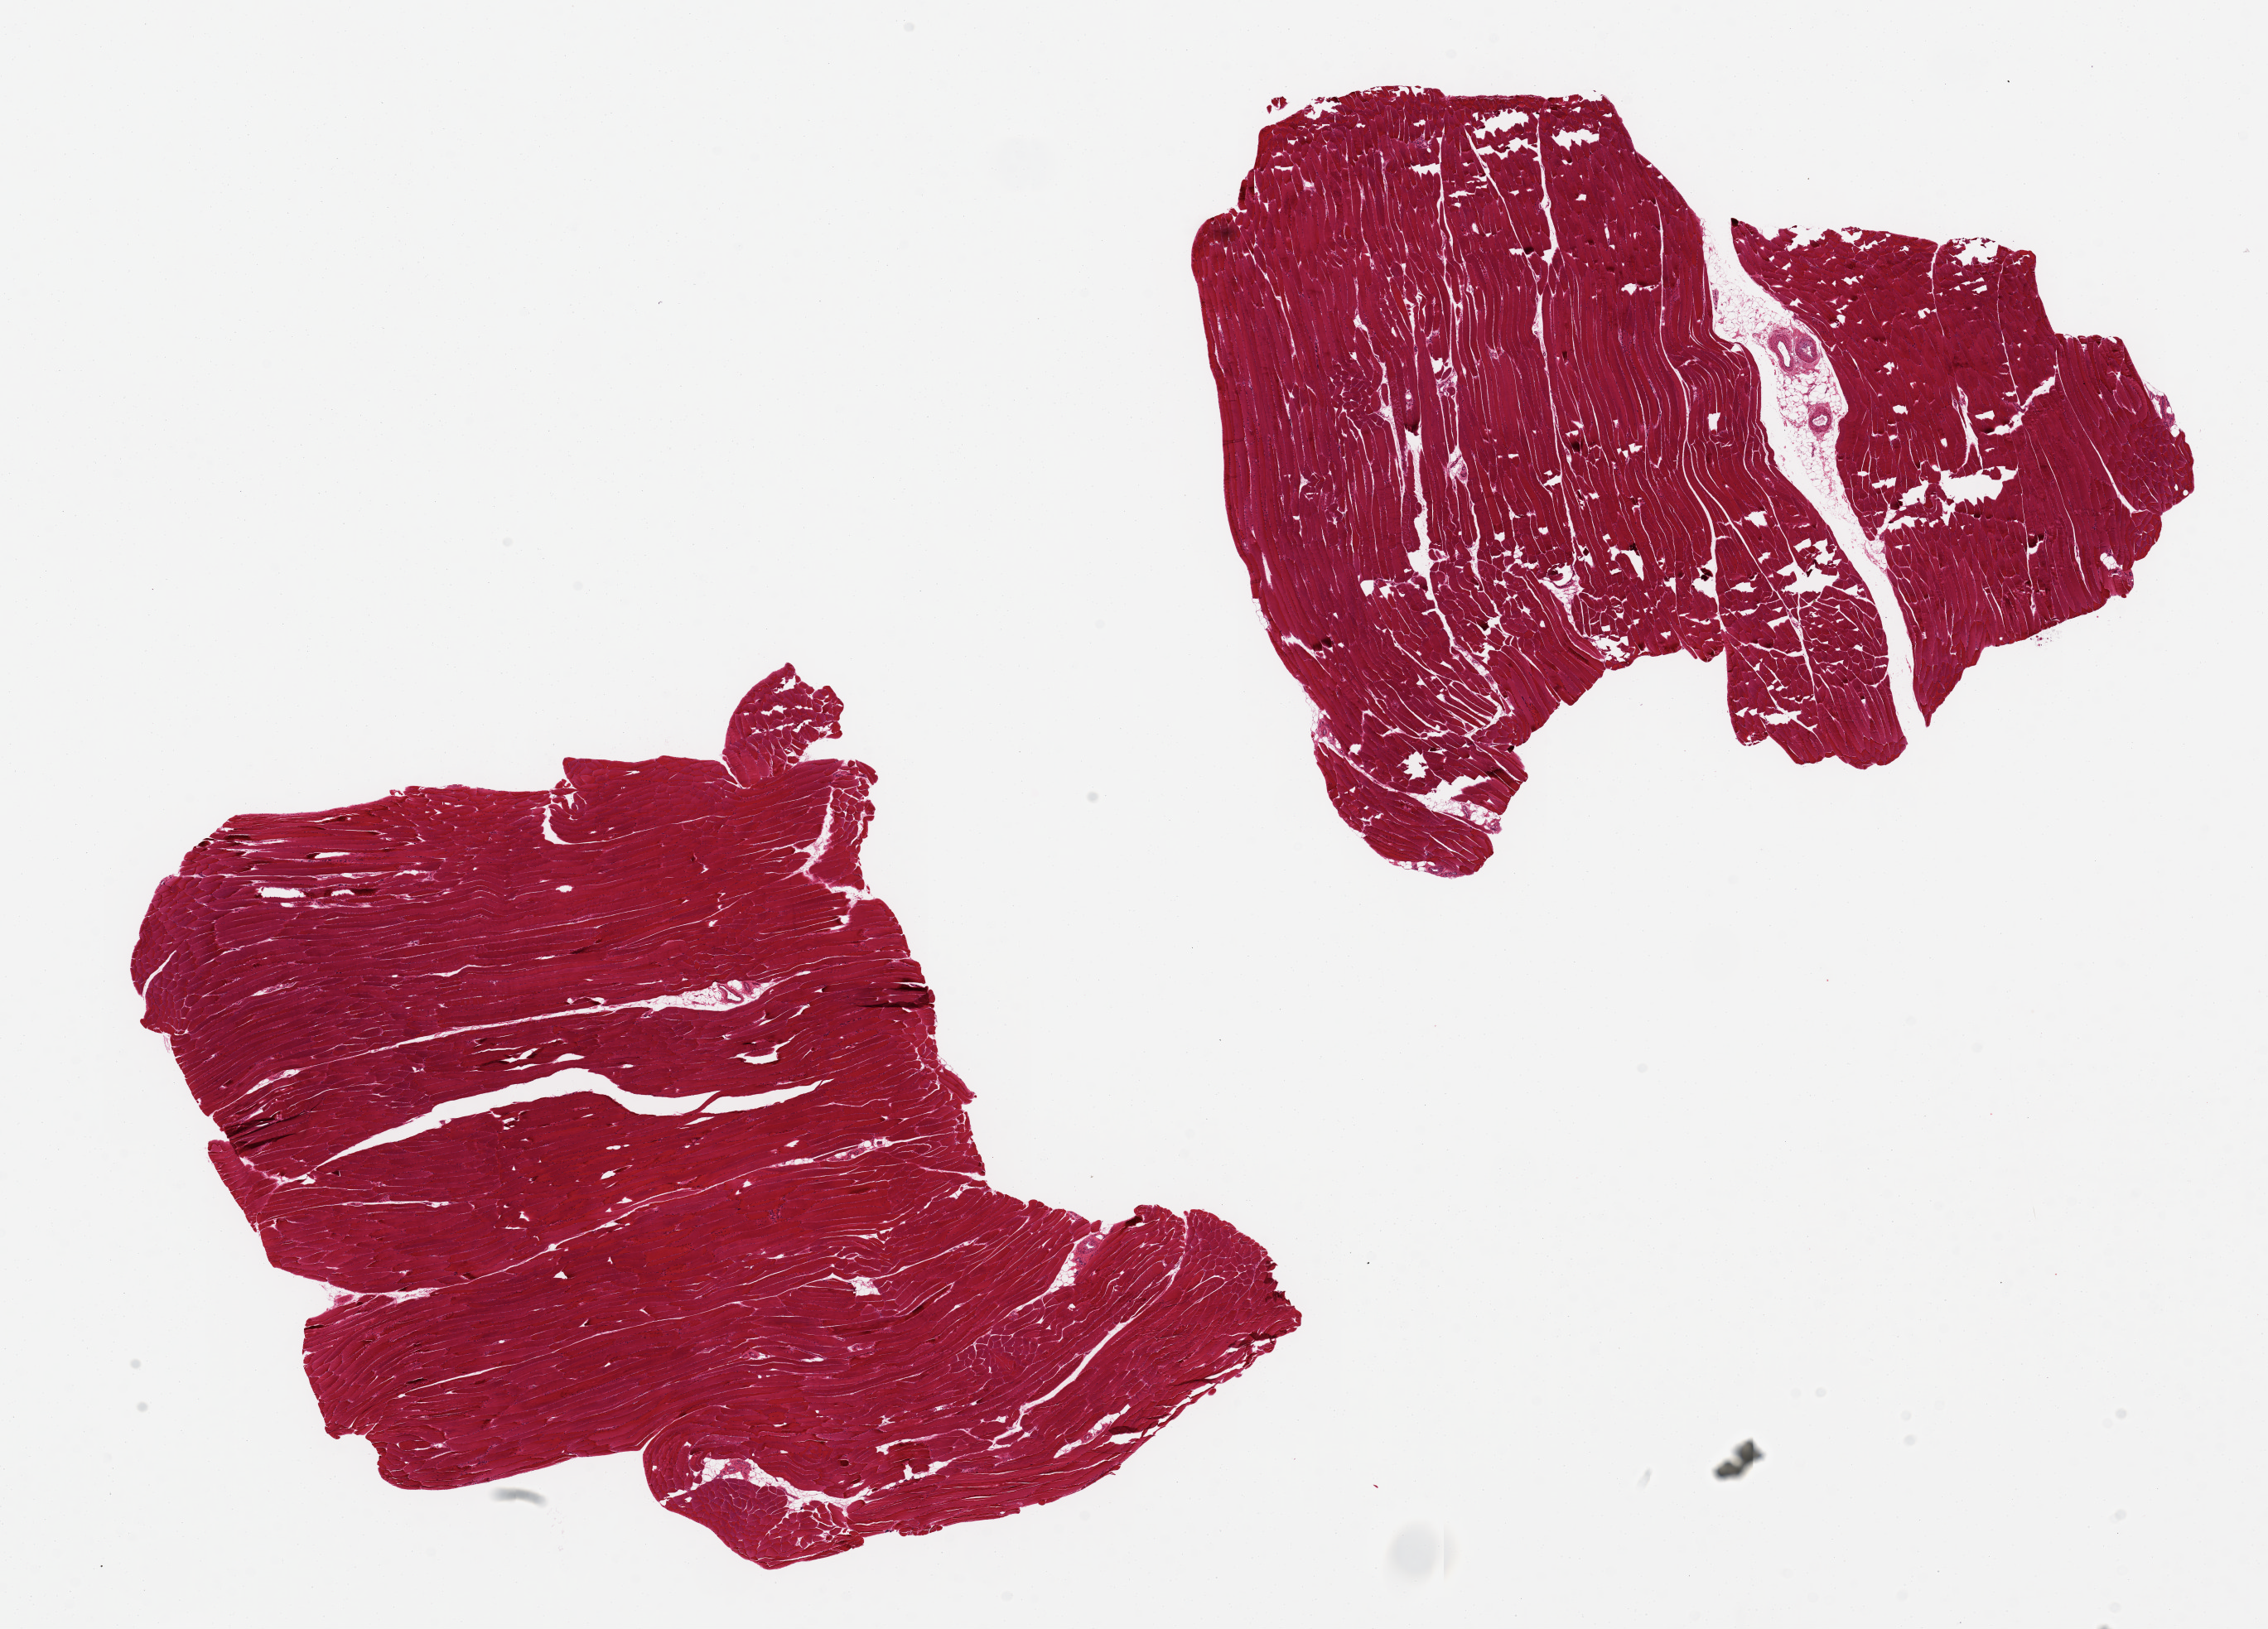
Digitized H&E-stained section — a low-resolution overview of the entire scanned area, about 21.7 x 15.6 mm. PAXgene-fixed, paraffin-embedded tissue. Target tissue: skeletal muscle. Donor tissue sample.
• reviewer comment on this tissue sample: 2 pieces, 9x7 & 9x8 mm